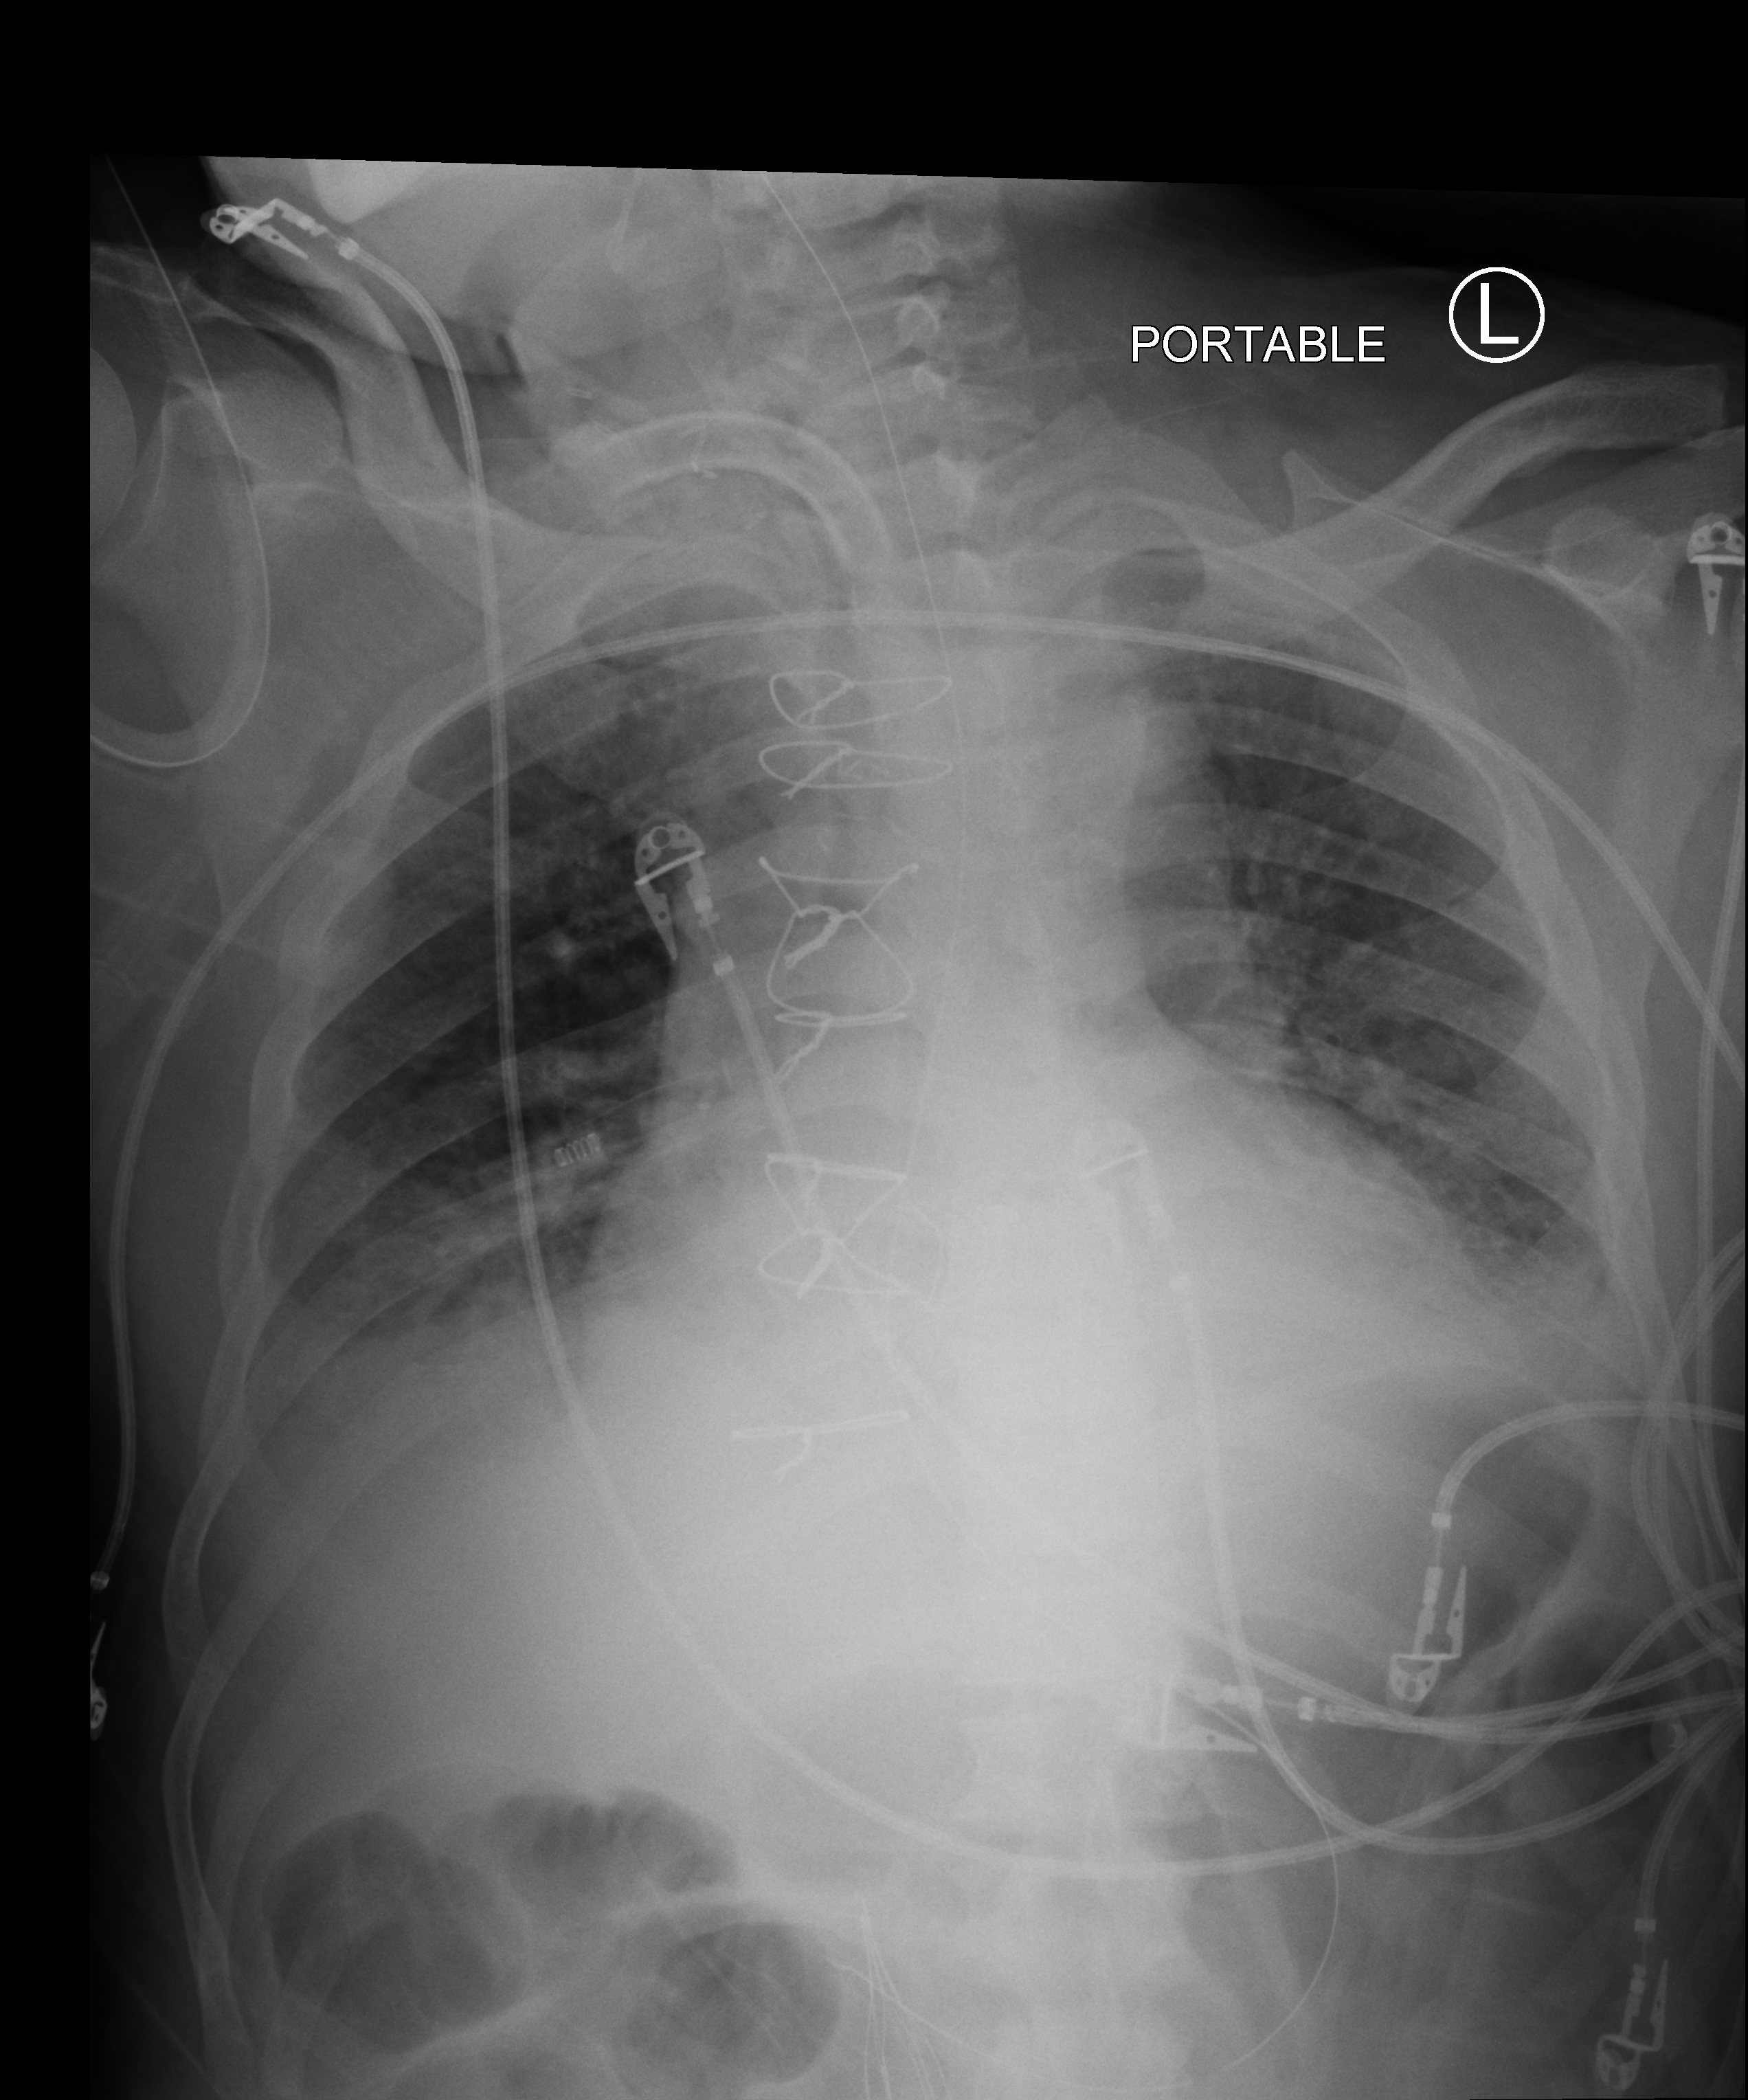
Chest X-ray (portable); anteroposterior (AP) projection. Male patient hospitalised with COVID-19, age 60–74 years.
Hospital-stay facts (about this admission, not read from this image; timing relative to this image not recorded): admitted to intensive care during this hospital stay: yes.